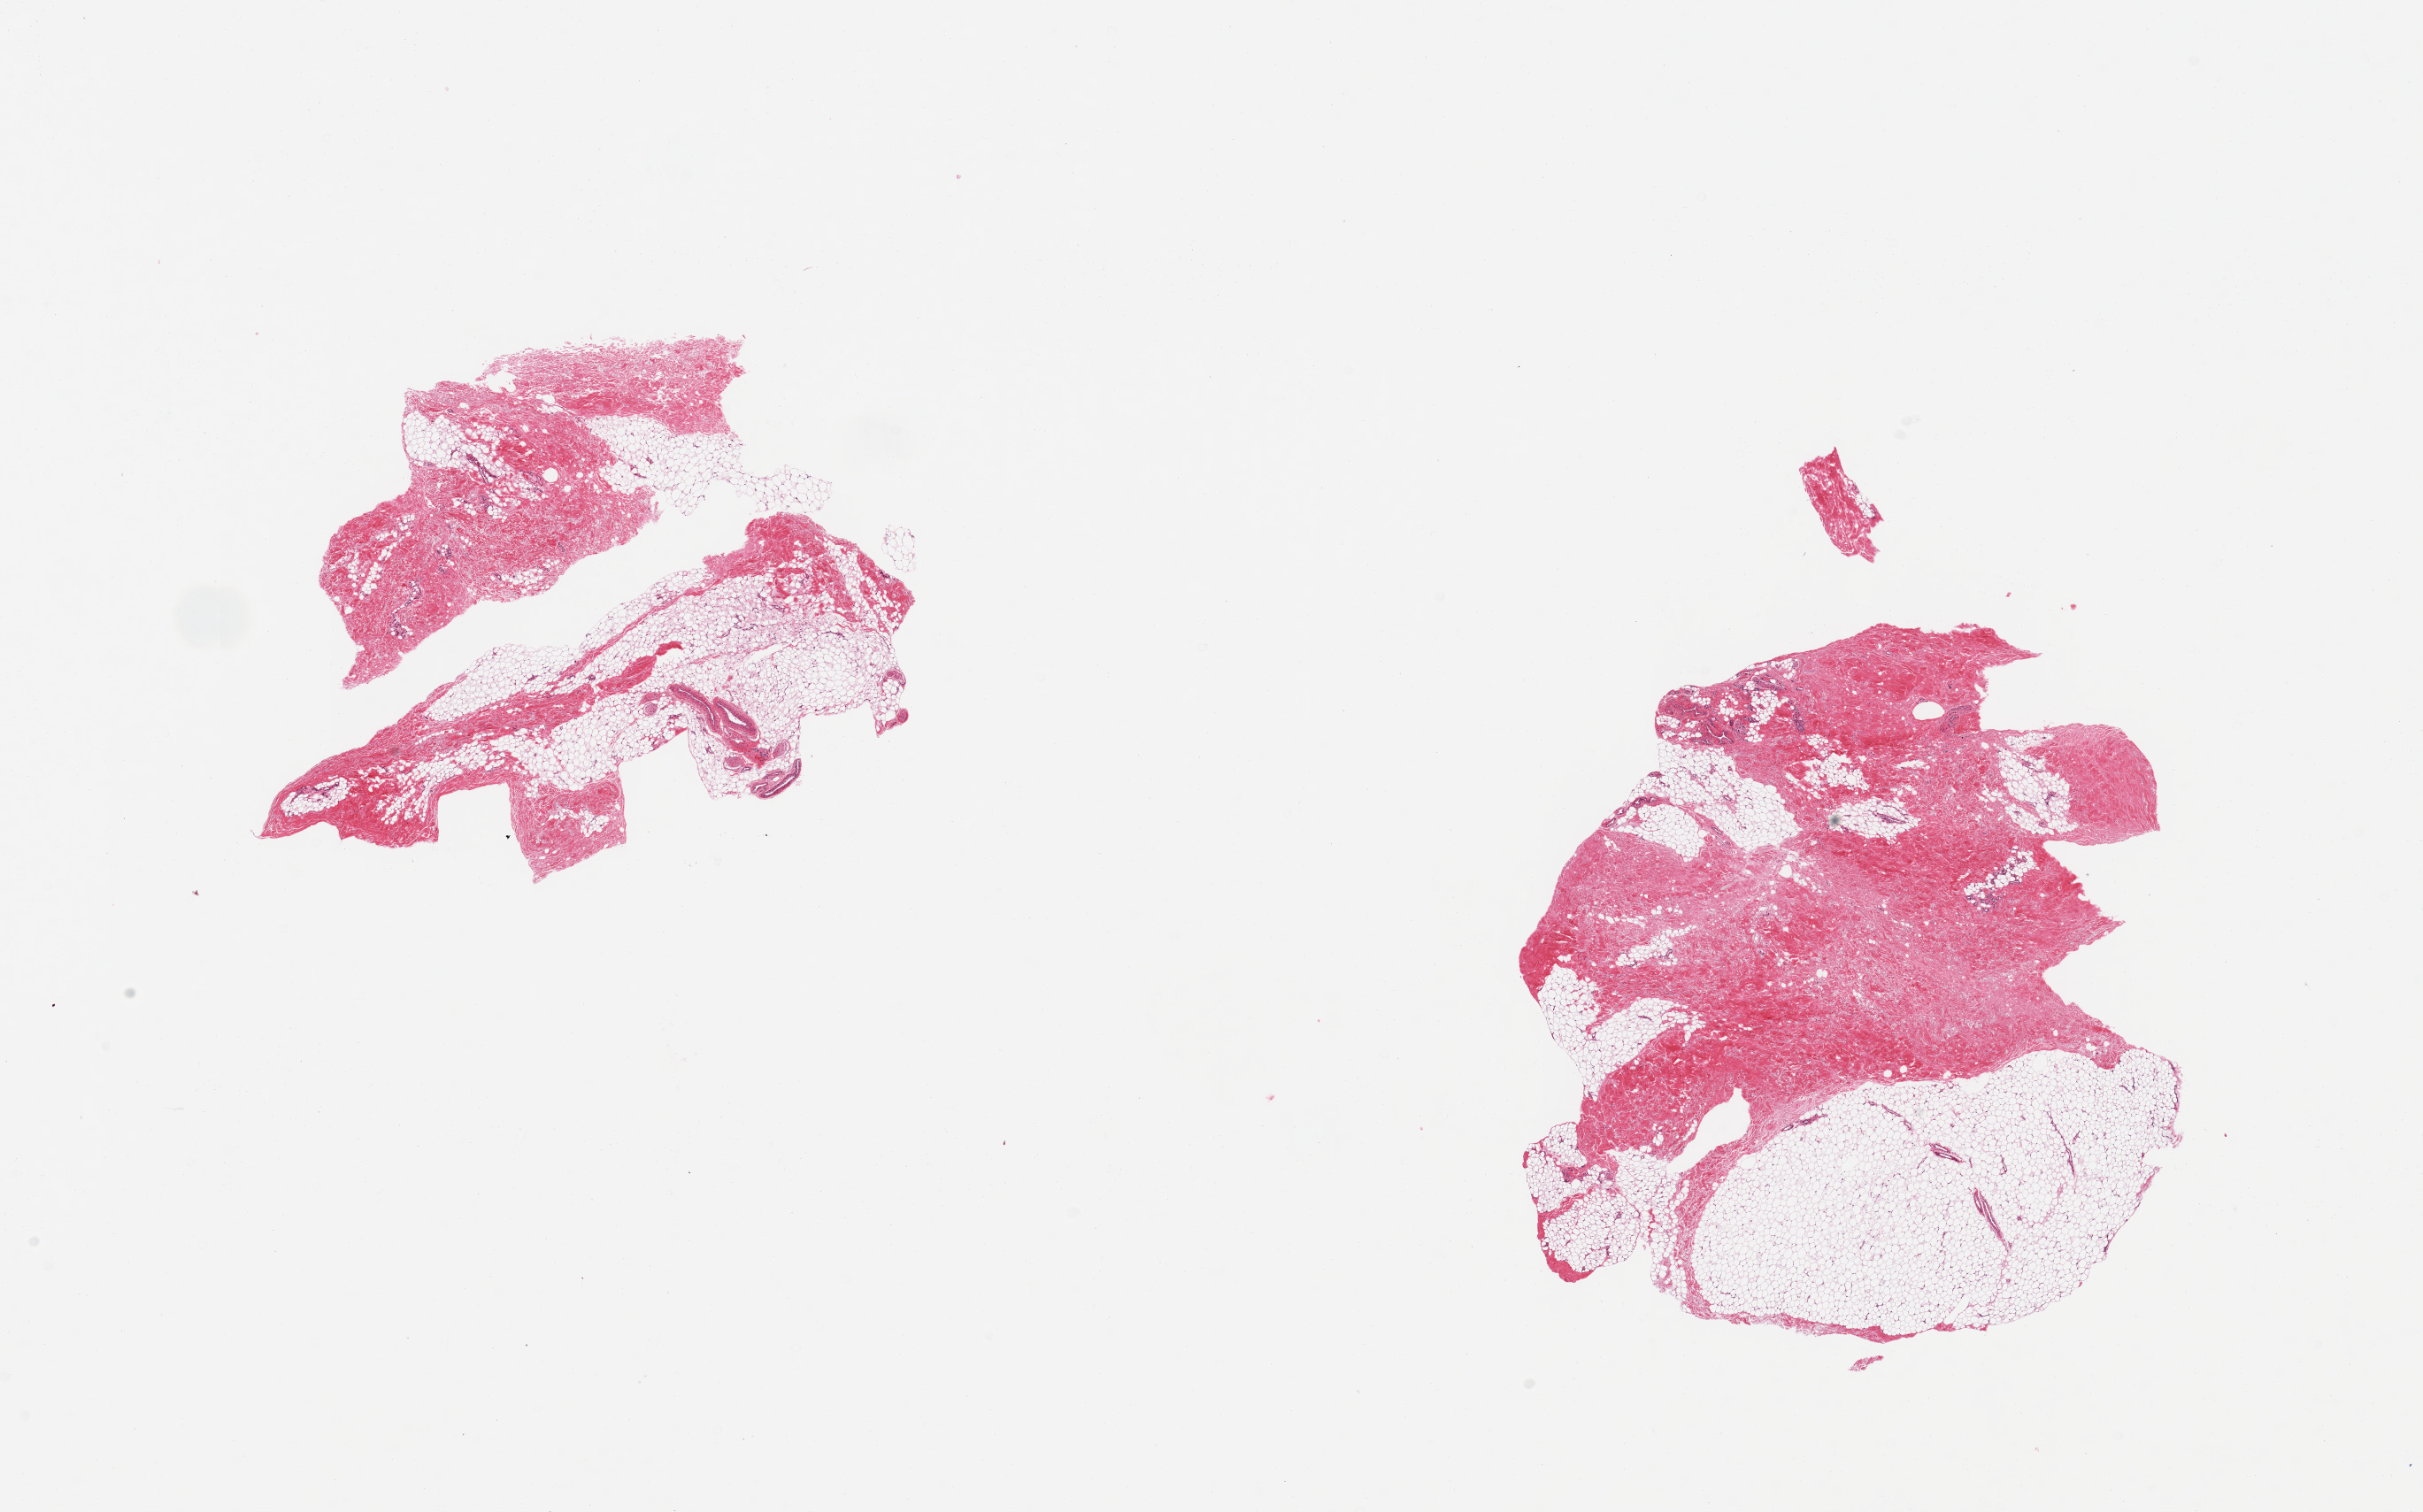
H&E whole-slide image, low-resolution overview of the scanned area, about 21.7 x 13.5 mm (slide scanned at 20x); PAXgene-fixed, paraffin-embedded tissue; sampled site (target tissue): breast; donor tissue sample.
Review note (as recorded): 2 pieces; one with 50% mature adipose tissue and 50% dense fibrovascular component; other with 40% adipose tissue and 60% fibrovascular component; no ductal elements present.